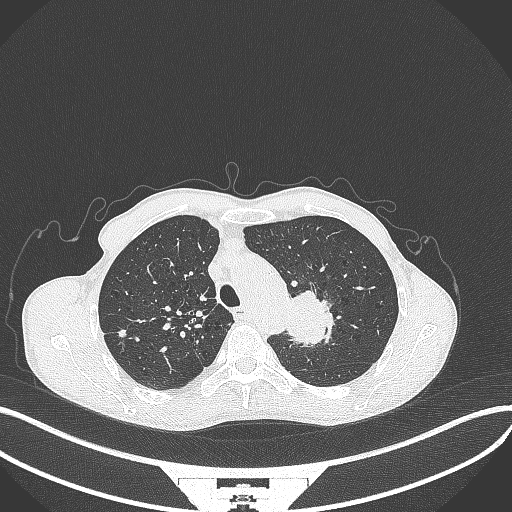
Chest CT, one axial slice; position 321 of 386 along the scan axis; reconstruction kernel B70f; 120 kVp; lung window (W 1500 / L -600 HU); 512 × 512 image matrix, field of view 400 × 400 mm. Patient: male, 65 years. Case-level facts recorded for this patient, not image findings: clinical TNM (as recorded): T2b N0 M0.
Structures marked on this image (rectangle marked by the reading radiologist):
- lung tumour (recorded histology: adenocarcinoma): bounding box [x1, y1, x2, y2] px = [286, 285, 337, 348]